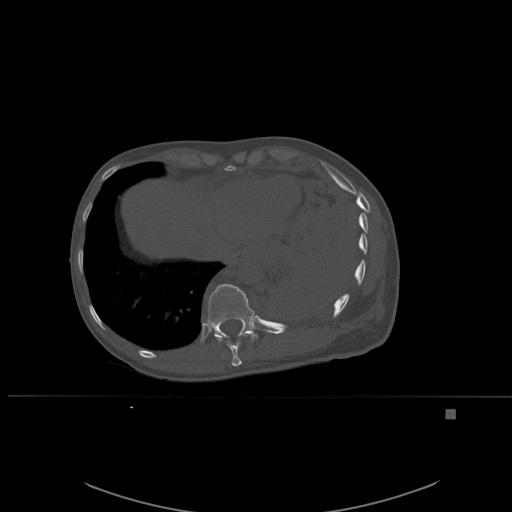
CT including the spine, one axial slice. Position 307 of 537 along the scan axis. Bone window (W 1800 / L 400 HU). 1.5 mm slice thickness. 512 × 512 image matrix, field of view 440 × 440 mm. Patient: female, 45 years. From the clinical record (not read from this slice): primary cancer: lung.
Outlined on this slice (semi-automatic segmentation, software-assisted and operator-edited):
- T10 vertebra: bounding box (x1, y1, x2, y2) in pixels: (214, 333, 248, 366)
- T11 vertebra: (207, 284, 258, 342)